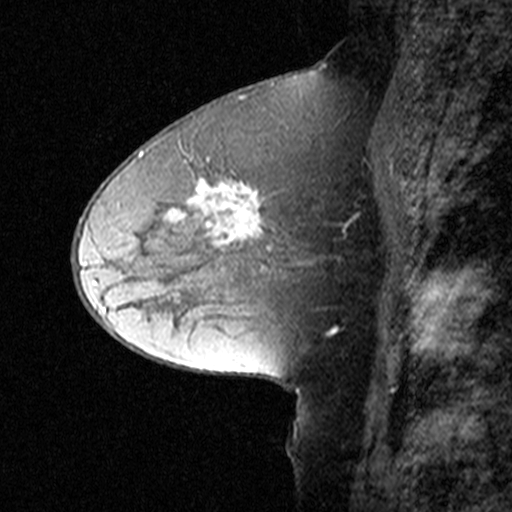
Breast MRI (dynamic contrast-enhanced), one sagittal slice; position 23 of 44 along the scan axis; dynamic contrast-enhanced study with each time point stored as its own series, time point 2 of 3 at this slice position (early post-contrast, ordered by acquisition time); 1.5 T; TE 4.5 ms, TR 11 ms; 512 × 512 image matrix, field of view 200 × 200 mm. Patient: female, 50 years. From the clinical record (not read from this slice): setting: breast cancer imaged before/during neoadjuvant chemotherapy; receptor status: HR-positive, HER2-negative.
Structures marked on this image (semi-automatically segmented with operator editing):
- analysis volume of interest (the breast-tissue region the enhancement analysis was run in; not a lesion): bounding box [x1, y1, x2, y2] px = [126, 162, 329, 291]
- tumour enhancement mask (voxels above the 90 % enhancement threshold inside the analysis volume of interest): [170, 181, 263, 246]